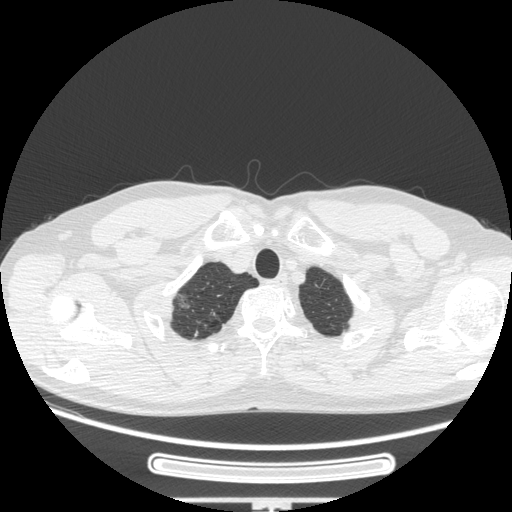
Chest CT, one axial slice; position 241 of 269 along the scan axis; reconstruction kernel STANDARD; lung window (W 1500 / L -600 HU); 1.25 mm slice thickness; 512 × 512 image matrix. Male patient, age 53 years. Case-level facts recorded for this patient, not image findings: clinical TNM (as recorded): T1c N0 M0; histopathological grade: G2.
Outlined on this slice (bounding box drawn by a radiologist):
- lung tumour (recorded histology: adenocarcinoma): bounding box <169,286,195,312> (left, top, right, bottom; pixels)